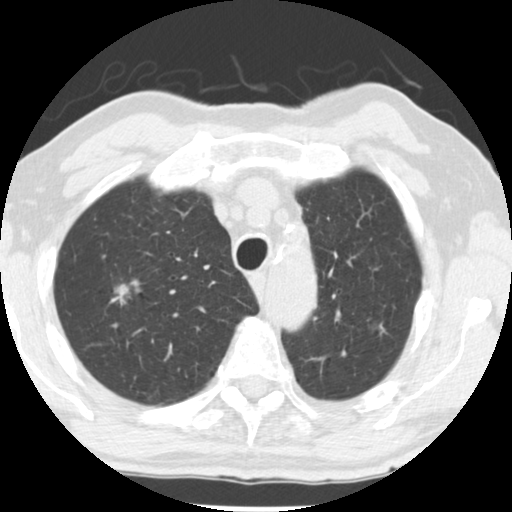
Low-dose screening chest CT, one axial slice; slice 200 of 252 in the series (ordered by position); reconstruction kernel STANDARD; lung window (W 1500 / L -600 HU); 2.5 mm slice thickness; 512 × 512 image matrix, field of view 313 × 313 mm.
Outlined on this slice (expert manual segmentation):
- lesion 1 (tumor, upper lobe of right lung): bounding box <114,280,140,303> (left, top, right, bottom; pixels)